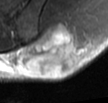
MRI of an extremity soft-tissue mass, one axial slice. Position 19 of 42 along the scan axis. T2-weighted fat-saturated. MR volume resampled by the dataset authors to the PET/CT grid (not the native acquisition matrix). 3.27 mm slice thickness. 108 × 103 image matrix. Male patient. Case-level facts recorded for this patient, not image findings: histological type: leiomyosarcoma; grade: intermediate; site of the primary tumour: left pelvis.
Outlined on this slice (expert contour drawn on MRI and transferred to this co-registered scan by the dataset authors):
- gross tumour volume (mass): bounding box (x1, y1, x2, y2) in pixels: (19, 23, 79, 77)